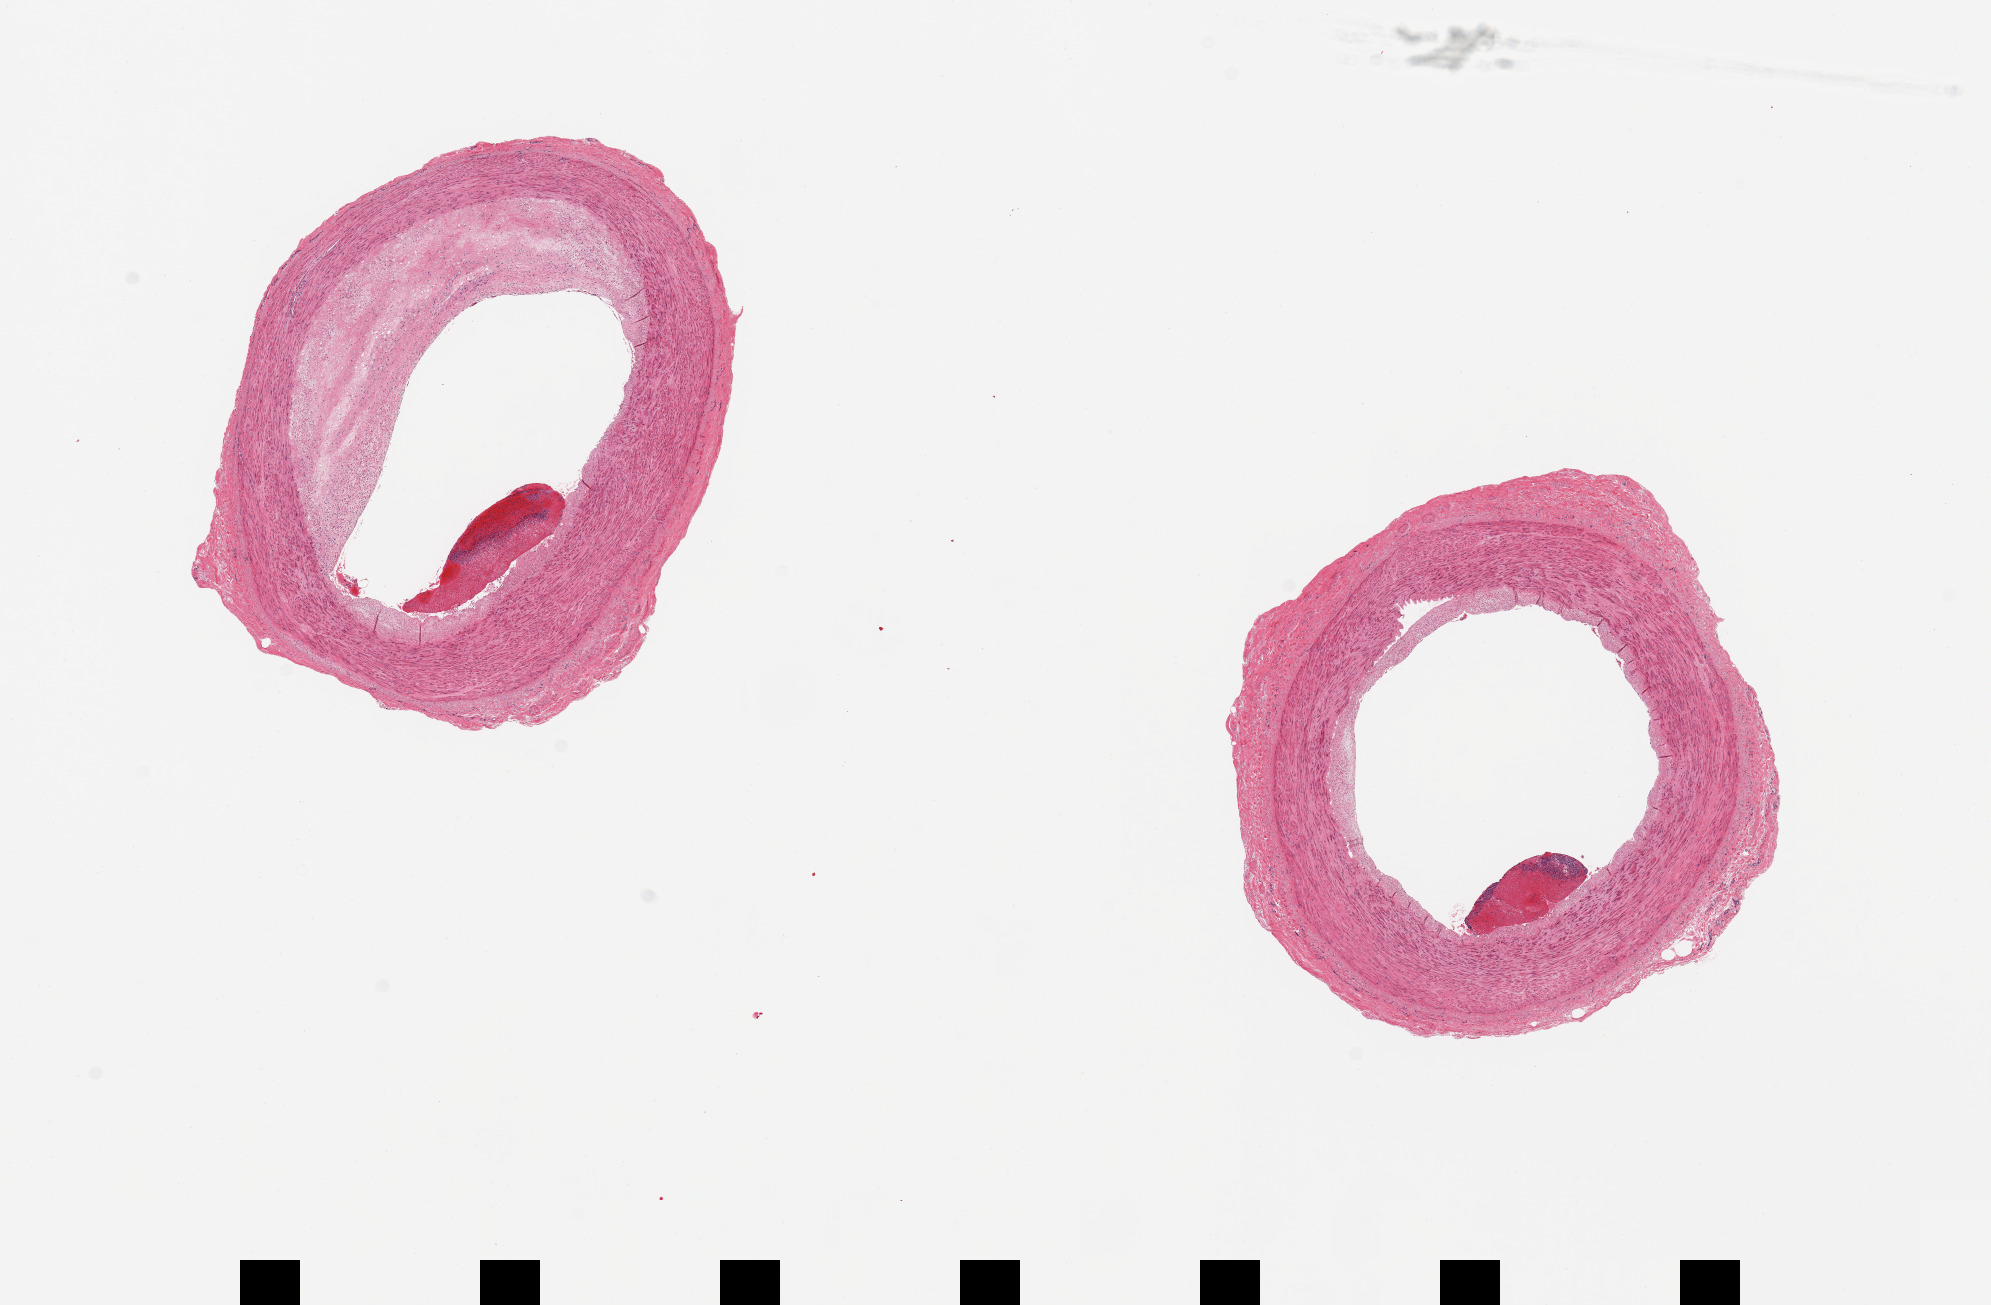
Digitized hematoxylin and eosin (H&E)-stained section, whole scanned area (about 15.8 x 10.3 mm) shown as a low-resolution overview, PAXgene-fixed, paraffin-embedded tissue, sampled site (target tissue): tibial artery, tissue donor sample. Donor: male.
Pathologist's review note for this sample: 2 pieces; atherosclerotic plaque 40% and 10%; blood clot in lumen; well trimmed.